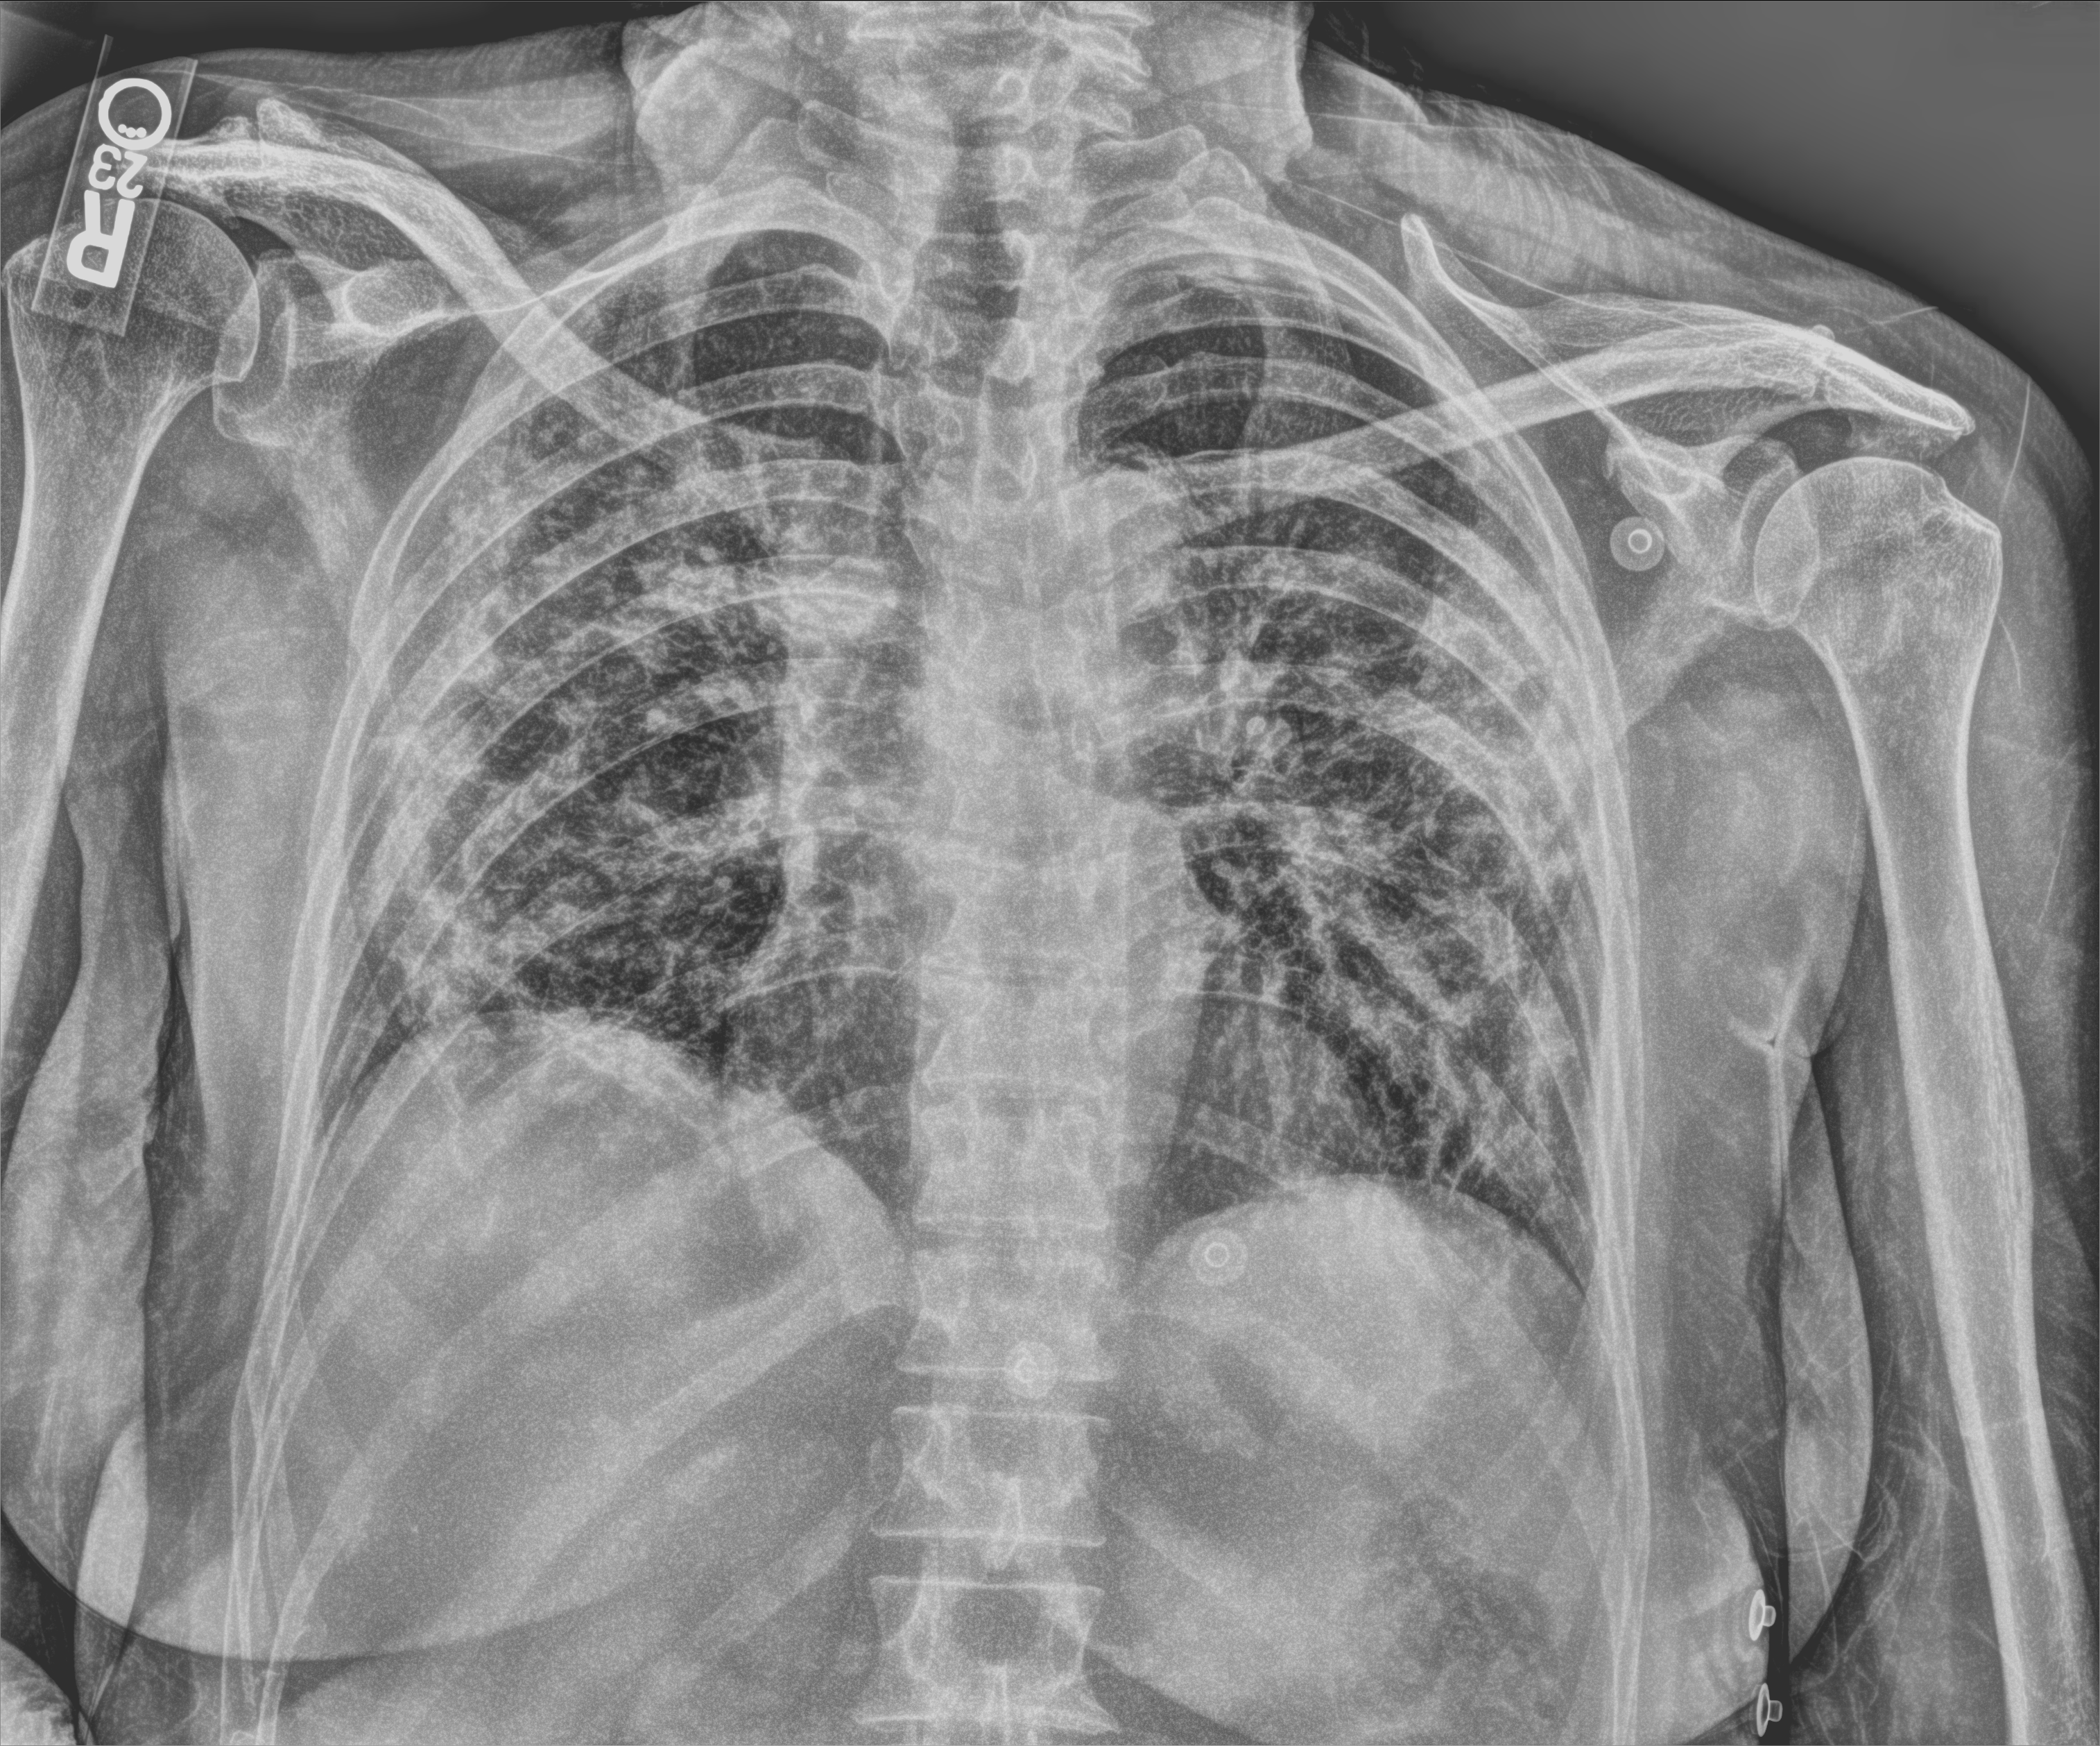
Bedside chest radiograph (computed radiography), anteroposterior (AP) projection. Patient hospitalised with COVID-19; female, aged 60–74 years.
Admission-level facts for this patient (not findings on this image; timing relative to this image not recorded): admitted to intensive care during this hospital stay: yes; hypertension (admission record): yes.